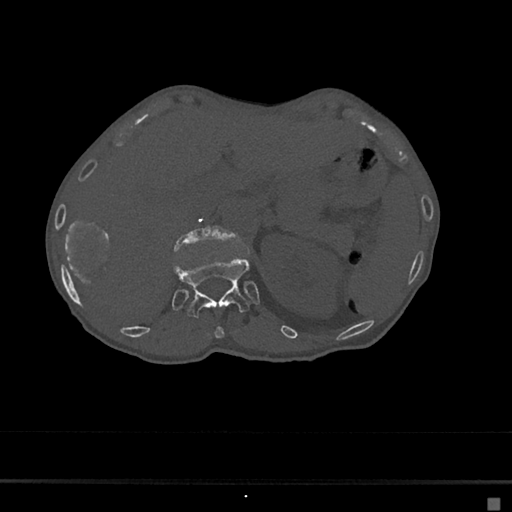
CT including the spine, one axial slice. Slice 122 of 797 in the series (ordered by position). Reconstruction kernel Br40s/3. Bone window (W 1800 / L 400 HU). 512 × 512 image matrix, field of view 360 × 360 mm. Female patient, age 68 years. From the clinical record (not read from this slice): primary cancer: renal.
Outlined on this slice (semi-automatically segmented with operator editing):
- L1 vertebra: bounding box [x1, y1, x2, y2] px = [175, 225, 232, 251]
- T11 vertebra: [214, 326, 224, 339]
- T12 vertebra: [173, 256, 250, 319]